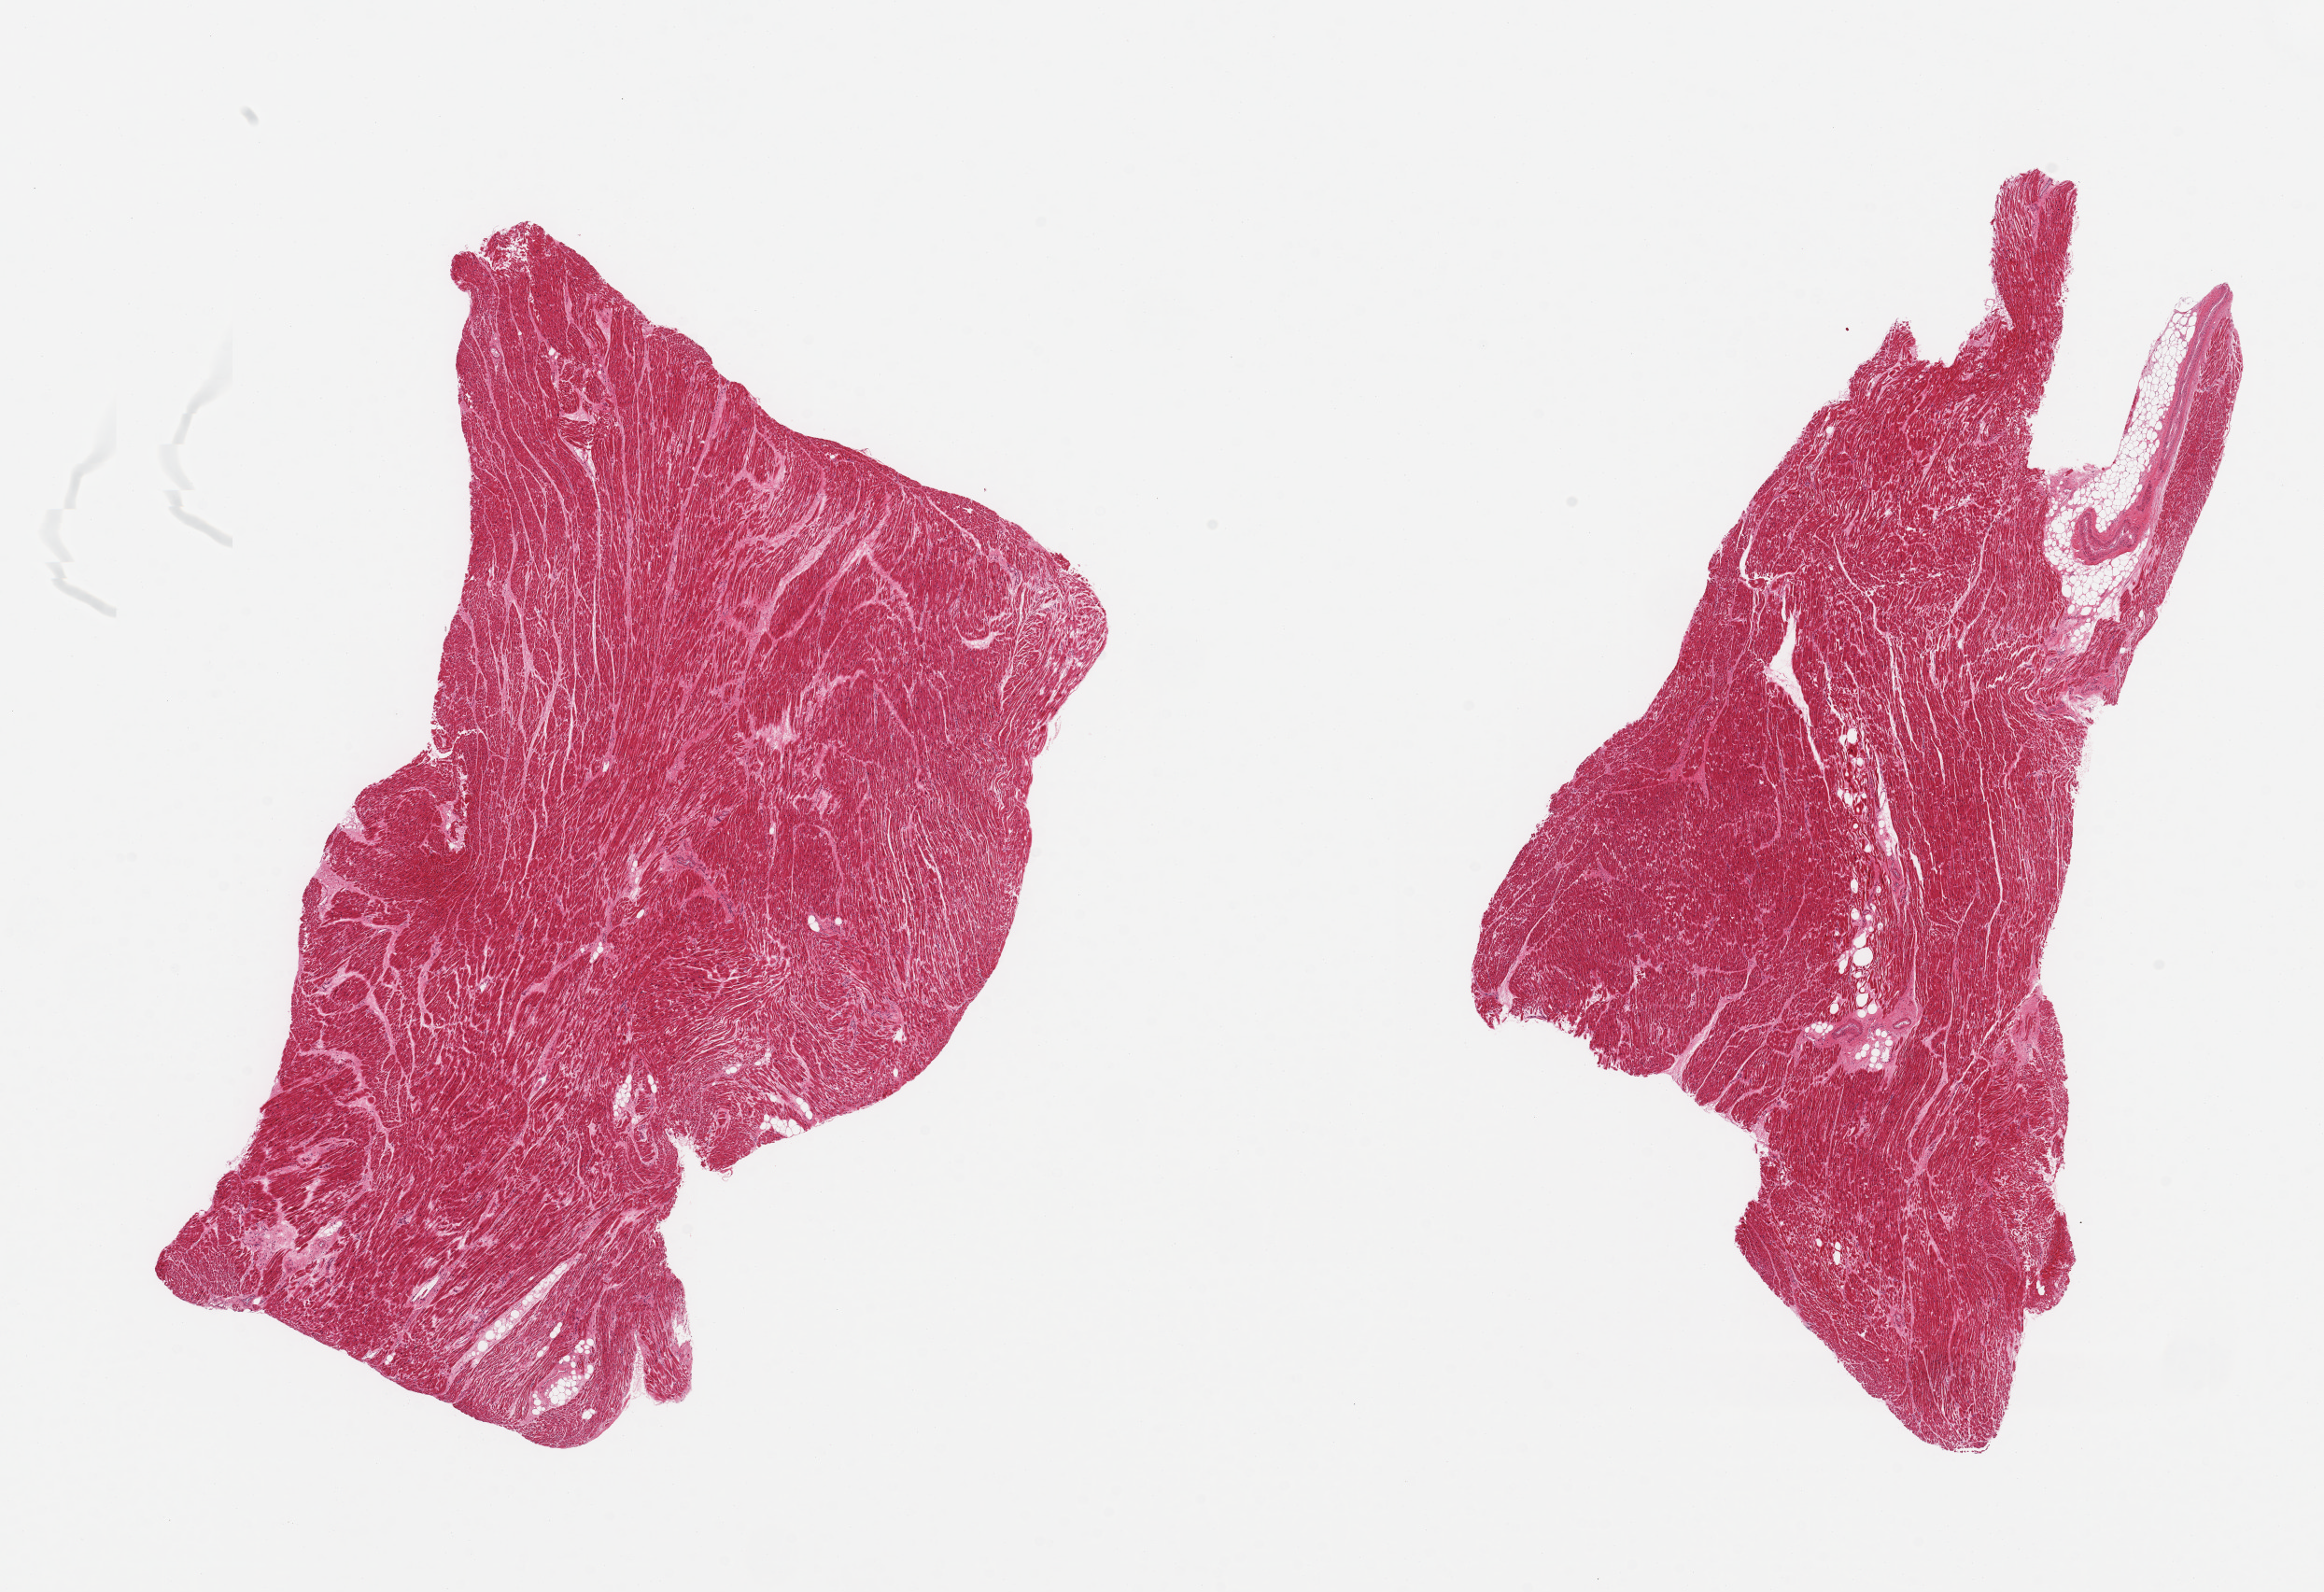
Whole-slide image, haematoxylin and eosin stain — low-resolution overview of the scanned area, about 19.7 x 13.5 mm, PAXgene-fixed, paraffin-embedded tissue, section of heart (target tissue), donor tissue sample. Female donor.
Review note (as recorded): 2 pieces mild chronic ischemic changes/interstitial fibrosis.